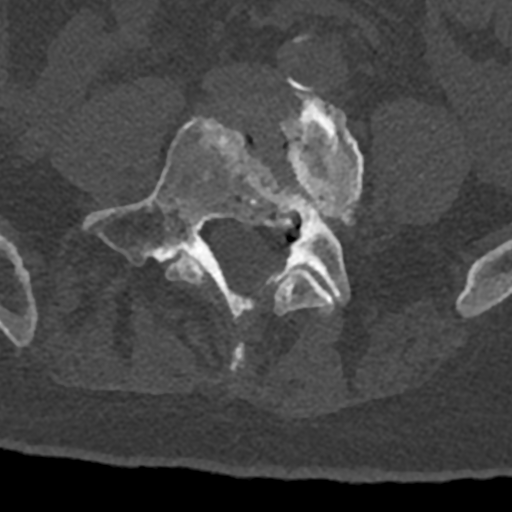
CT including the spine, one axial slice. Position 221 of 797 along the scan axis. Reconstruction kernel Br40s/3. Bone window (W 1800 / L 400 HU). 0.5 mm slice thickness. 512 × 512 image matrix, field of view 160 × 160 mm. Male patient, age 74 years. Case-level facts recorded for this patient, not image findings: primary cancer: renal.
Outlined on this slice (semi-automatic segmentation, software-assisted and operator-edited):
- L4 vertebra: bounding box (x1, y1, x2, y2) in pixels: (166, 82, 364, 371)
- L5 vertebra: (83, 116, 350, 317)